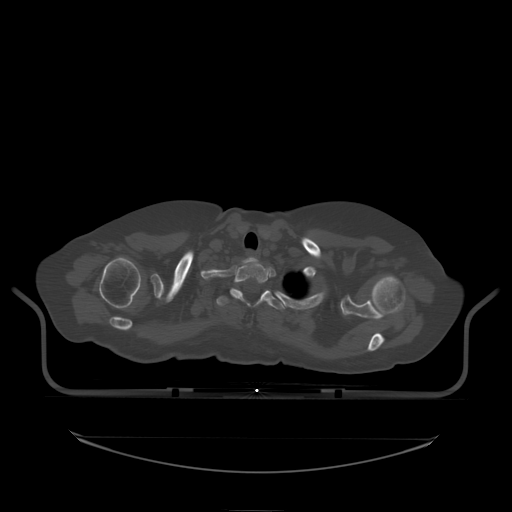
CT including the spine, one axial slice; position 184 of 242 along the scan axis; bone window (W 1800 / L 400 HU); 2.5 mm slice thickness; 512 × 512 image matrix, field of view 500 × 500 mm. Patient: female, 53 years. From the clinical record (not read from this slice): primary cancer: lung.
Outlined on this slice (semi-automatically segmented with operator editing):
- T1 vertebra: bounding box <232,265,270,301> (left, top, right, bottom; pixels)
- T2 vertebra: <217,289,286,310>